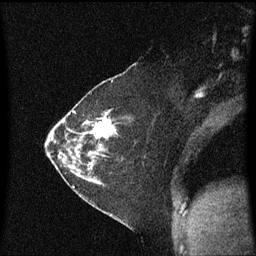
Breast MRI (dynamic contrast-enhanced), one sagittal slice. Position 36 of 60 along the scan axis. Dynamic contrast-enhanced series, image 2 of 3 at this slice position (ordered by acquisition). 1.5 T. TE 4.2 ms, TR 8.4 ms. 256 × 256 image matrix, field of view 200 × 200 mm. Patient: female, 36 years. From the clinical record (not read from this slice): setting: breast cancer imaged before/during neoadjuvant chemotherapy; receptor status: HR-positive, HER2-negative.
Structures marked on this image (semi-automatically segmented with operator editing):
- analysis volume of interest (the breast-tissue region the enhancement analysis was run in; not a lesion): bounding box <66,102,119,179> (left, top, right, bottom; pixels)
- tumour enhancement mask (voxels above the 70 % enhancement threshold inside the analysis volume of interest): <85,112,117,165>